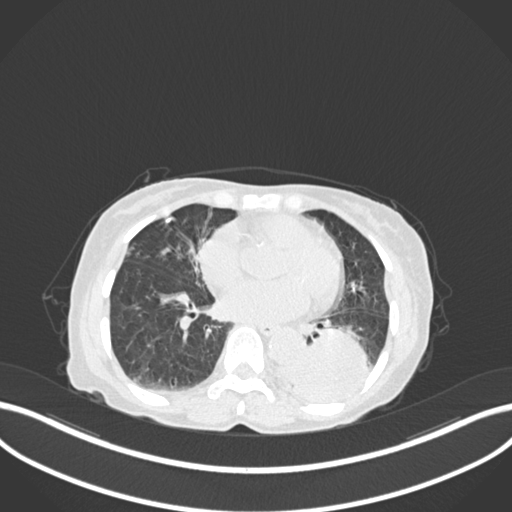
Chest CT, one axial slice. Slice 56 of 233 in the series (ordered by position). Reconstruction kernel B30f. Lung window (W 1500 / L -600 HU). 512 × 512 image matrix. Patient: female, 78 years. Case-level facts recorded for this patient, not image findings: clinical TNM (as recorded): T3 N0 M1.
Outlined on this slice (rectangle marked by the reading radiologist):
- lung tumour (recorded histology: squamous cell carcinoma): box from (x=285, y=321) to (x=373, y=407) px